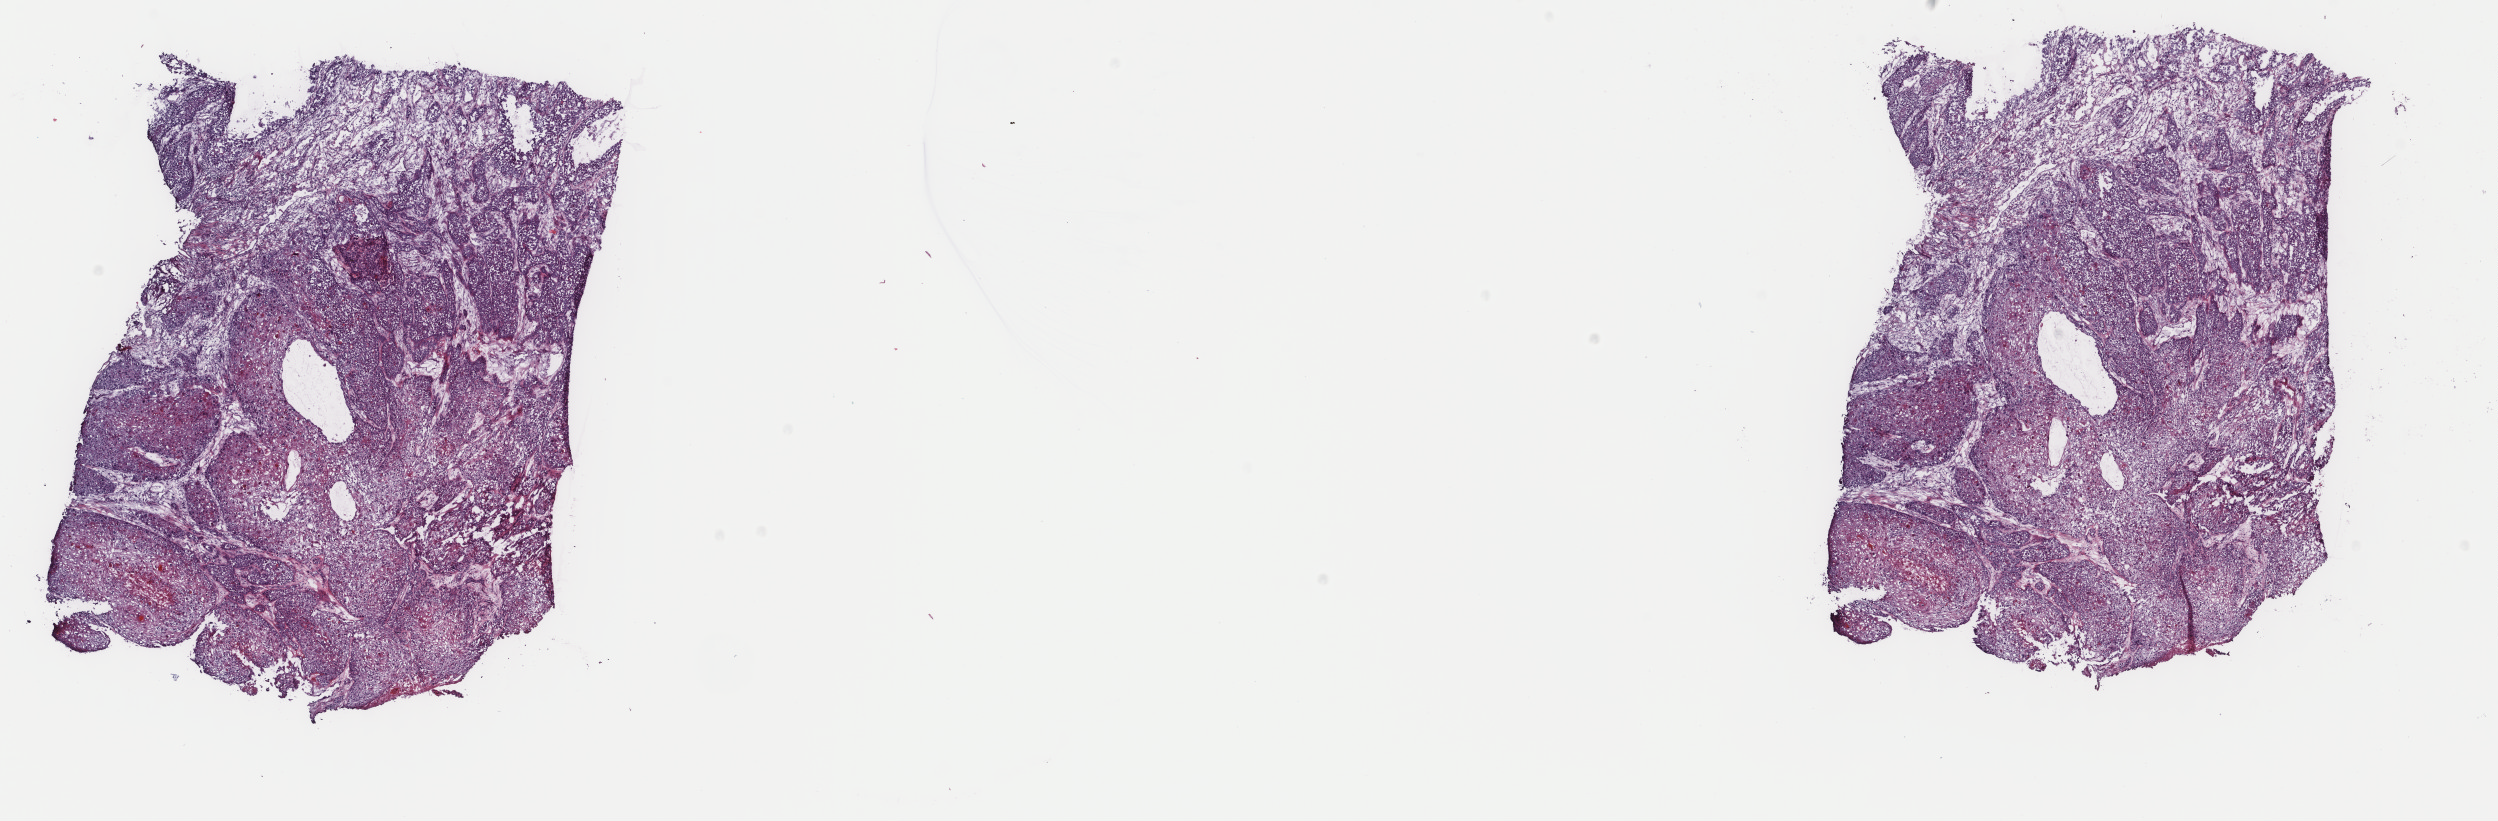
Digitized H&E tissue section (whole slide), whole scanned area (about 19.8 x 6.5 mm, acquisition: 40x scan) shown as a low-resolution overview. Frozen section from the top of the tissue portion. Primary tumour sample from the head and neck. Female patient; age at initial diagnosis 53 years. Histologic grade: G2 (moderately differentiated). Slide review estimates, as recorded: tumour cells 90%, tumour nuclei 90%, normal cells 0%, stromal cells 10%, necrosis 0%. Inflammatory infiltration, as recorded: lymphocyte infiltration 10%, monocyte infiltration 0%, neutrophil infiltration 0%.
• AJCC pathologic stage: IVA
• TNM: T4 N0 MX
• diagnosis: Squamous cell carcinoma, keratinizing, NOS (floor of mouth, NOS)